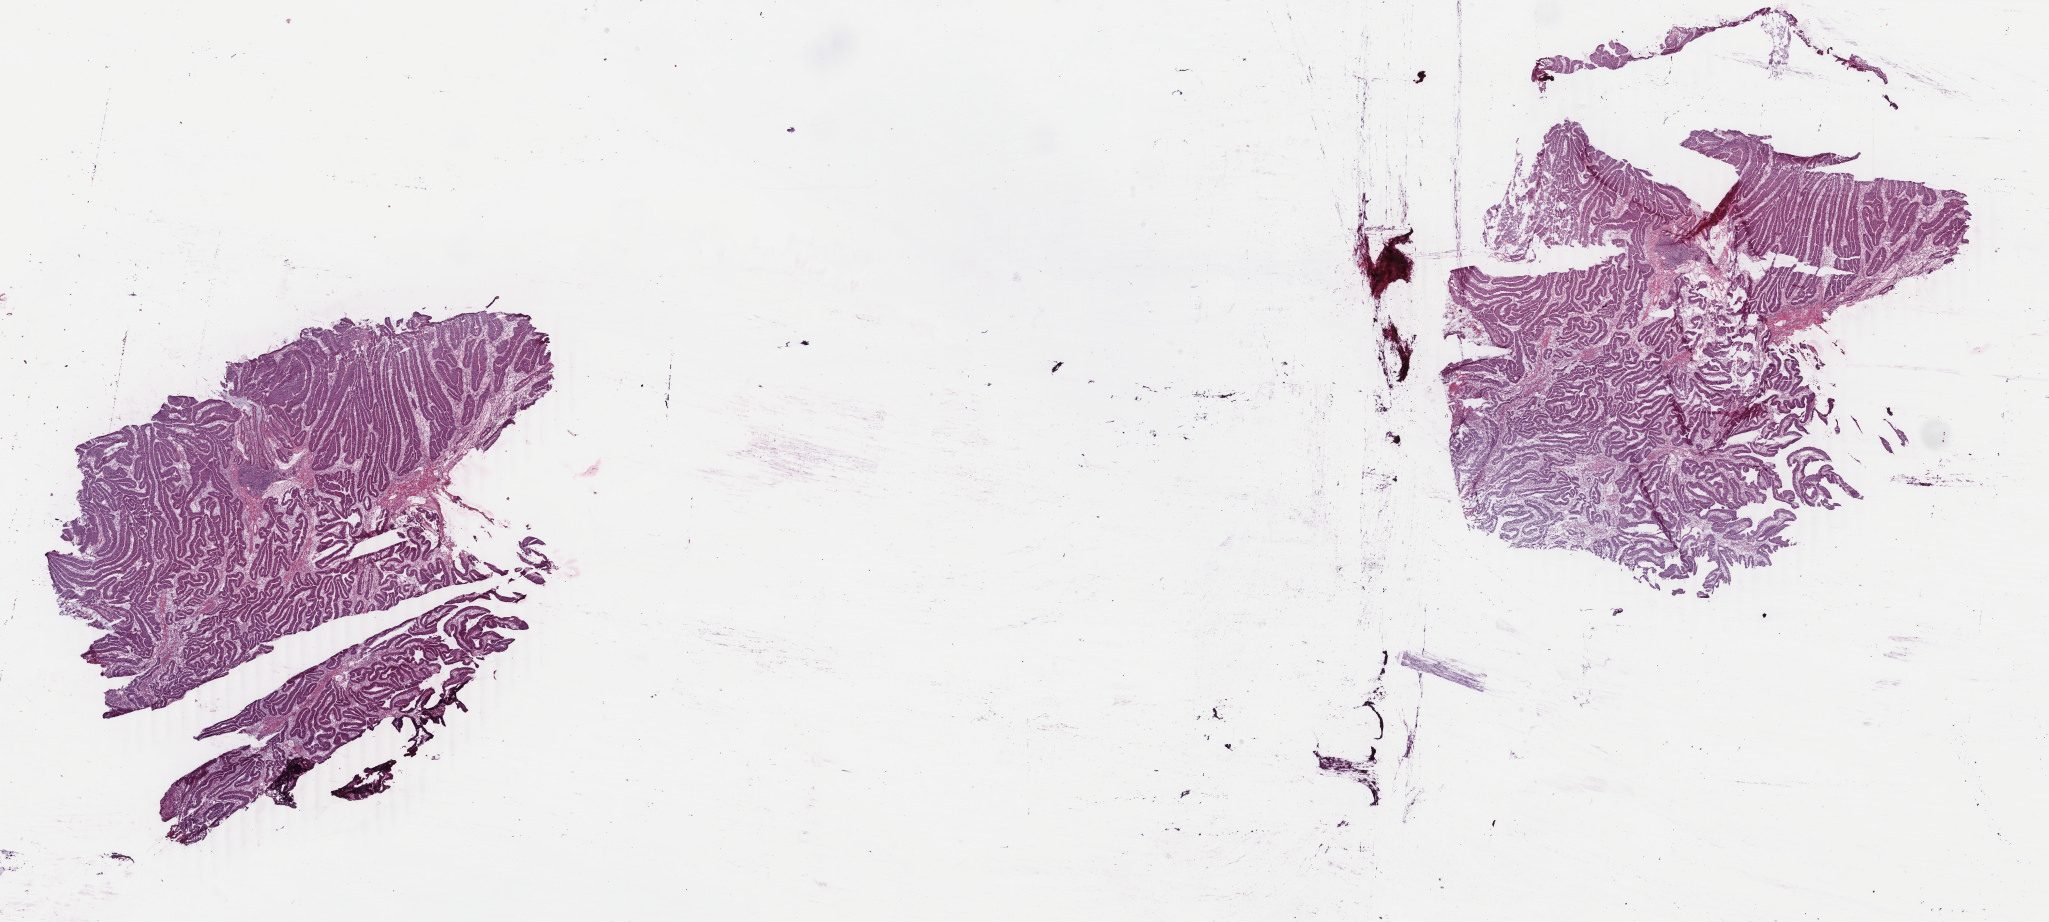
Whole-slide histology image, H&E-stained, whole scanned area (about 32.6 x 14.7 mm) shown as a low-resolution overview; frozen section; sample: primary tumour, rectum. Patient: male, age at initial diagnosis 77 years. Slide review estimates, as recorded: tumour cells 85%, tumour nuclei 80%, normal cells 5%, stromal cells 8%, necrosis 2%. Infiltration values recorded for this section: lymphocyte infiltration 8%, monocyte infiltration 2%, neutrophil infiltration 2%.
TNM: T2 N0 M0. Diagnosis: Adenocarcinoma, NOS. AJCC pathologic stage: I (6th edition).